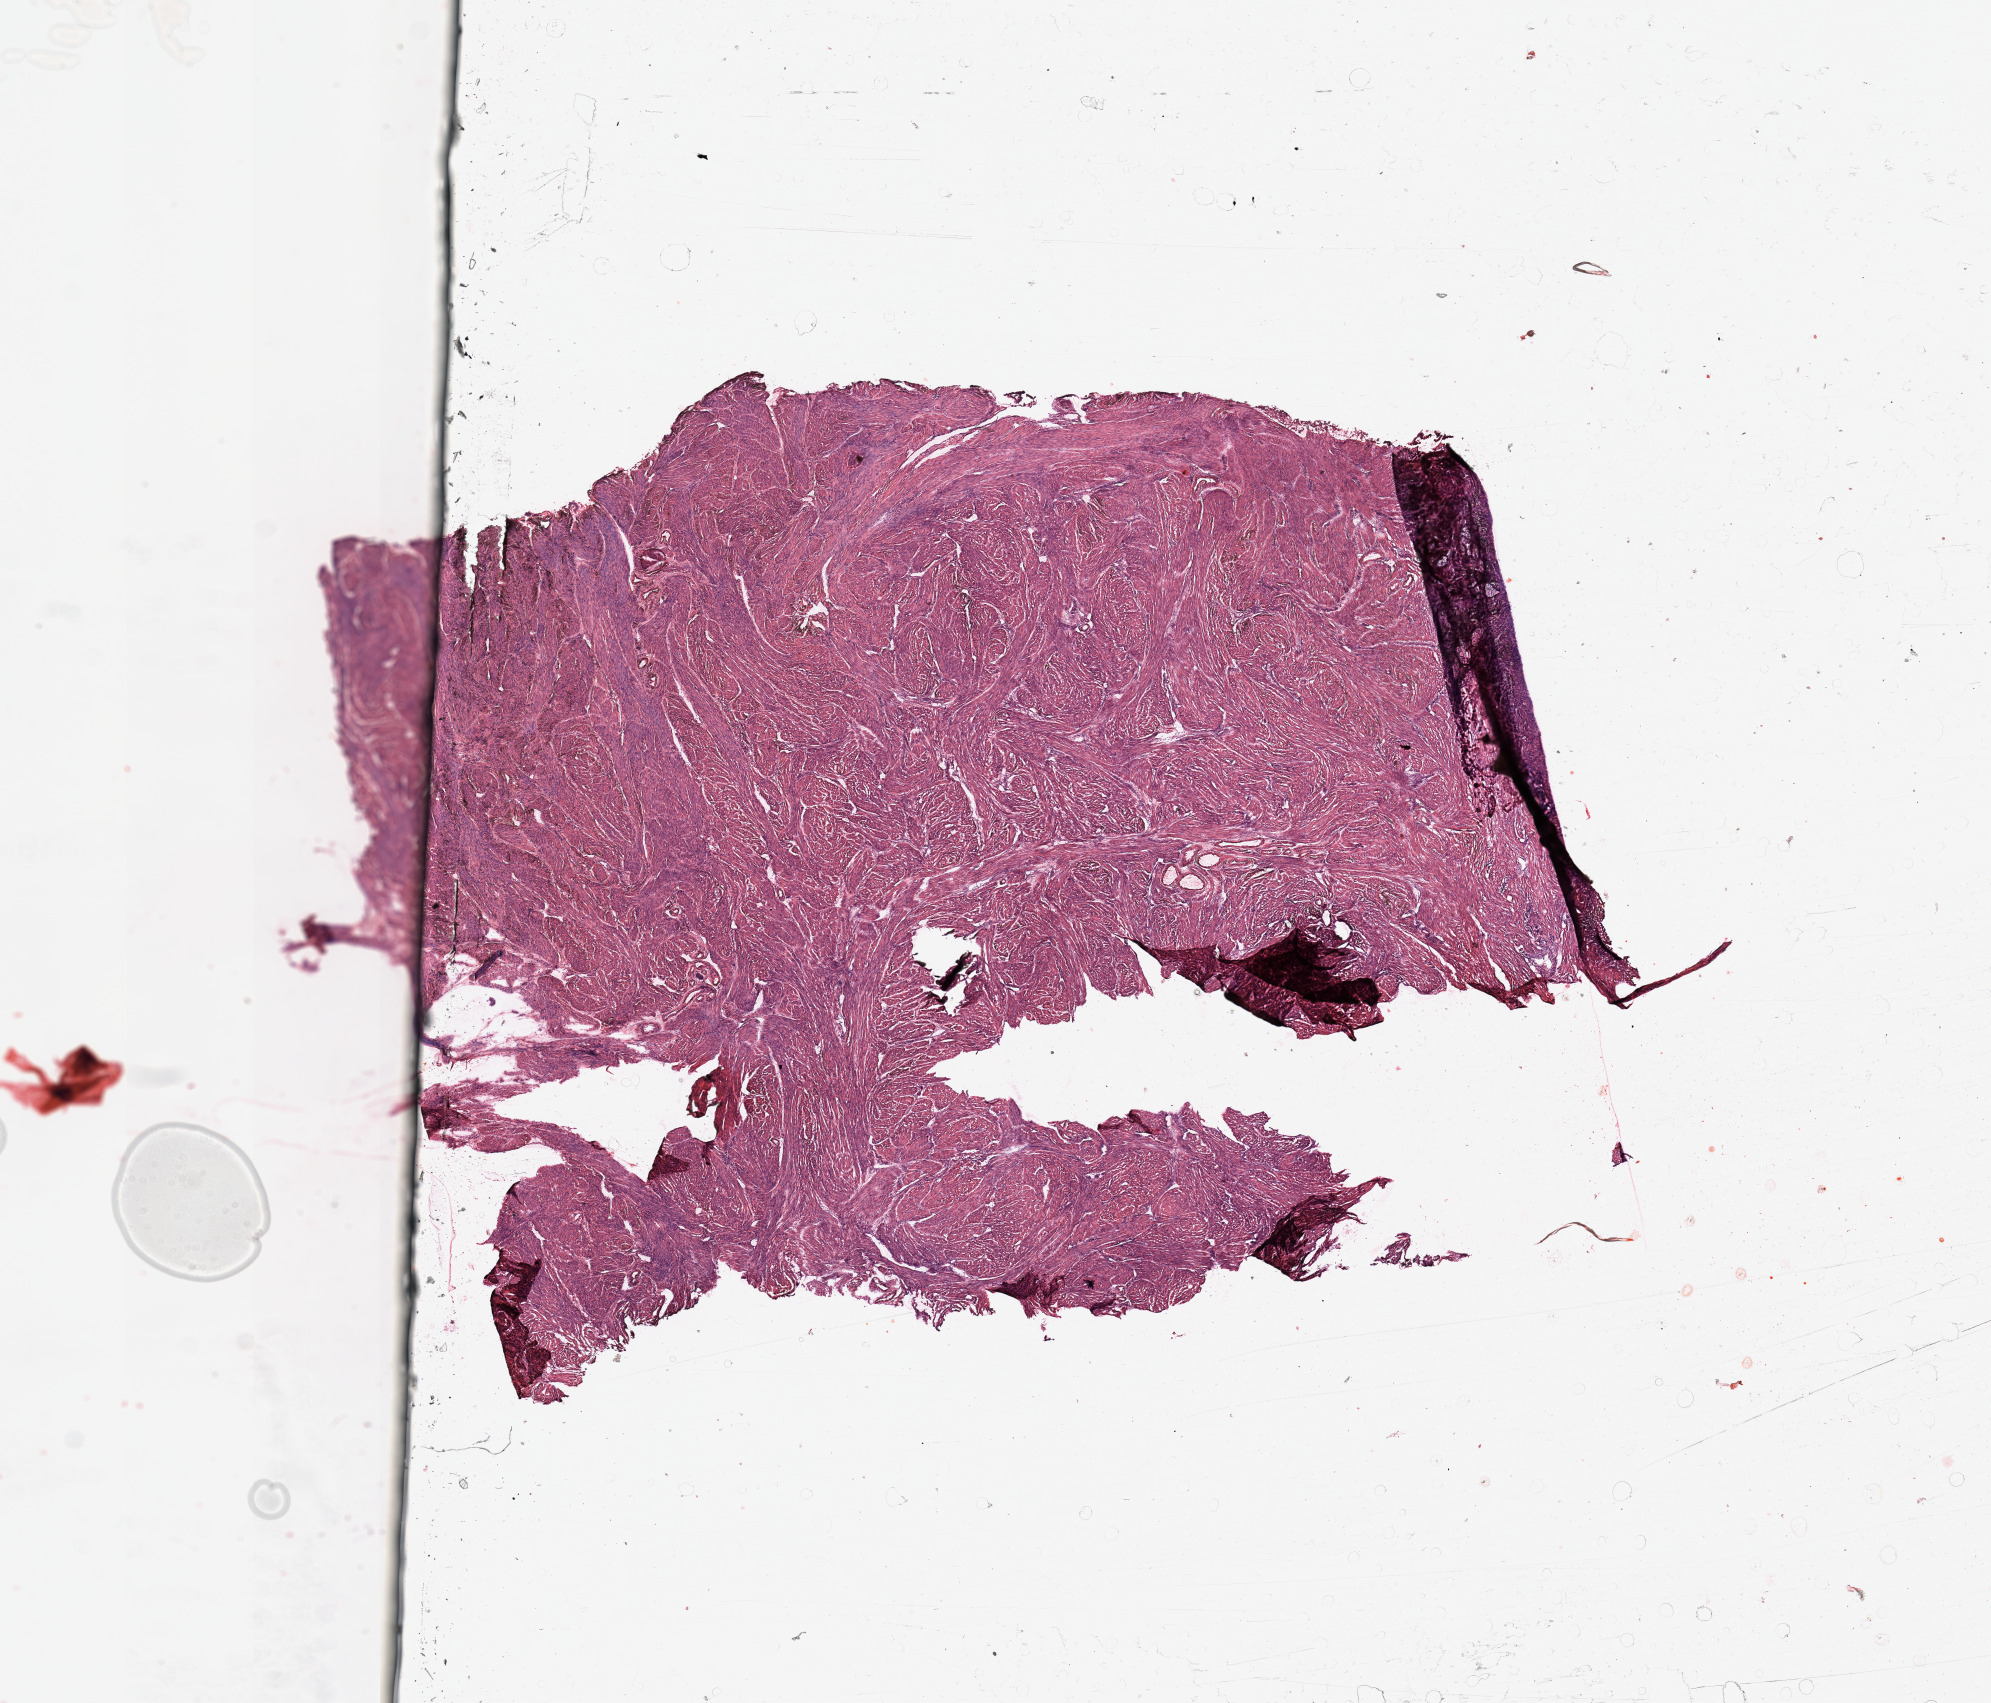
Whole-slide histology image, H&E-stained, whole scanned area (about 15.8 x 13.5 mm, slide scanned at 20x) shown as a low-resolution overview. Uterus, normal (non-tumour) tissue. Patient: female, age 61 years.
This section: normal (non-tumour) tissue from the same patient. Patient diagnosis: Endometrioid adenocarcinoma, NOS.